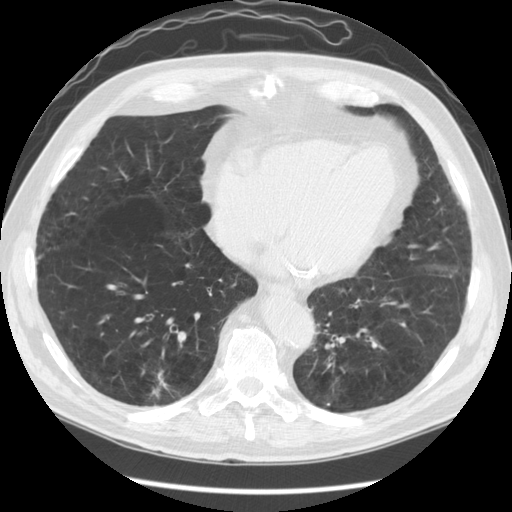
Axial slice from a low-dose chest CT screening exam, baseline annual screen, lung window (W 1500 / L -600 HU), slice 94 of 141 in the series. Male participant, aged 67 years at enrolment. Former smoker at enrolment.
Expert-annotated lung lesion, bounding box <119,356,189,420> (left, top, right, bottom; pixels). The screening reader recorded 2 non-calcified nodules or masses ≥4 mm on this exam (right lower lobe, right lower lobe); which of them this box marks is not recorded. Later outcome: lung cancer diagnosed 78 days after this screen — squamous cell carcinoma, NOS, right lower lobe, moderately differentiated (G2), stage IA (AJCC 6th edition), 23 mm at pathology.